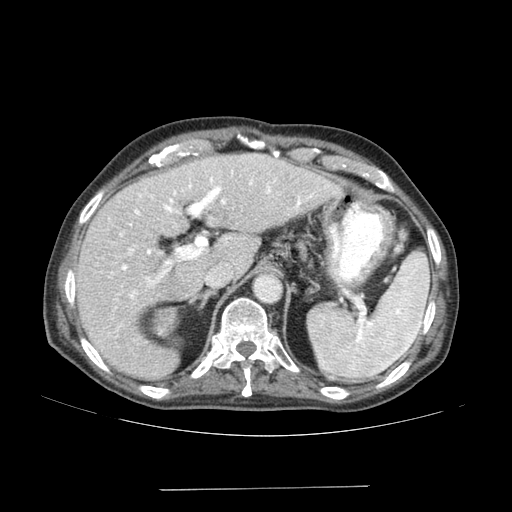
Contrast-enhanced abdominal CT (liver protocol), one axial slice. Position 110 of 192 along the scan axis. Reconstruction kernel SOFT. Soft-tissue window (W 400 / L 40 HU). 512 × 512 image matrix, field of view 400 × 400 mm. From the clinical record (not read from this slice): diagnosis: hepatocellular carcinoma (patient treated with transarterial chemoembolisation; whether this scan precedes or follows treatment is not stated here); TNM stage (as recorded): Stage-IVA; Child-Pugh class: A; tumour nodularity: uninodular.
Outlined on this slice (semi-automatically segmented with operator editing):
- liver parenchyma outside the tumour (the mass and vessels are separate outlines, so this box may not span the whole liver): box from (x=76, y=154) to (x=343, y=380) px
- liver vessels: (x=120, y=171)–(x=313, y=299)